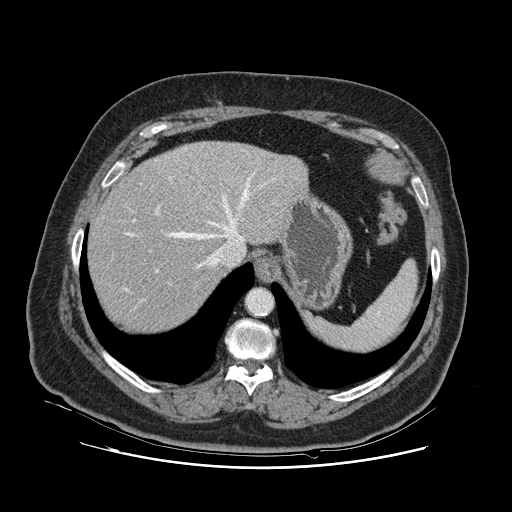
Contrast-enhanced abdominal CT, one axial slice. Slice 97 of 132 in the series (ordered by position). Intravenous contrast given. Soft-tissue window (W 400 / L 40 HU). 2.5 mm slice thickness. 512 × 512 image matrix, field of view 391 × 391 mm. Female patient, age 73 years. From the clinical record (not read from this slice): diagnosis: colorectal cancer liver metastases, imaged before liver resection; multiple liver metastases: no; largest metastasis: 7 cm; disease in both lobes: no.
Structures marked on this image (outlined manually by an expert reader):
- hepatic veins: bounding box [x1, y1, x2, y2] px = [123, 174, 254, 302]
- liver: [89, 143, 306, 333]
- planned liver remnant (the part of the liver to remain after resection): [89, 161, 227, 334]
- portal vein (with intrahepatic branches): [155, 205, 160, 273]